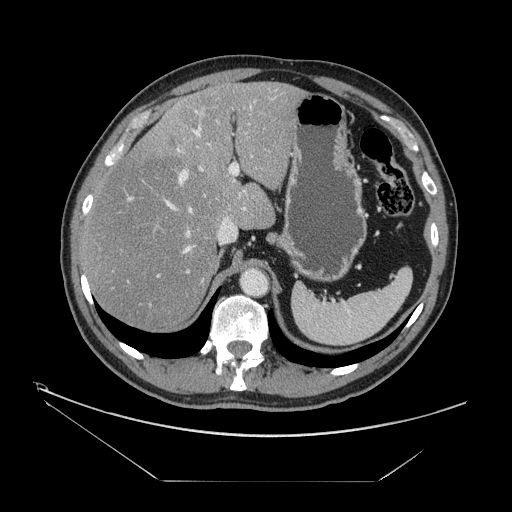
Contrast-enhanced abdominal CT, one axial slice. Slice 105 of 161 in the series (ordered by position). 120 kVp. Intravenous contrast given. Soft-tissue window (W 400 / L 40 HU). 2.5 mm slice thickness. 512 × 512 image matrix. Male patient, age 65 years. From the clinical record (not read from this slice): diagnosis: colorectal cancer liver metastases, imaged before liver resection; multiple liver metastases: yes; largest metastasis: 4.2 cm; disease in both lobes: yes.
Outlined on this slice (expert manual segmentation):
- hepatic veins: box from (x=128, y=127) to (x=210, y=282) px
- liver: (x=83, y=82)–(x=301, y=329)
- planned liver remnant (the part of the liver to remain after resection): (x=82, y=82)–(x=301, y=329)
- portal vein (with intrahepatic branches): (x=111, y=90)–(x=277, y=307)
- liver metastasis: (x=170, y=138)–(x=178, y=147)